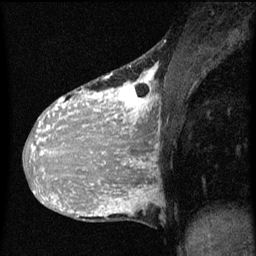
Breast MRI (dynamic contrast-enhanced), one sagittal slice; slice 26 of 60 in the series (ordered by position); dynamic contrast-enhanced series, image 2 of 3 at this slice position (ordered by acquisition); 1.5 T; TE 4.2 ms, TR 8 ms; 2 mm slice thickness; 256 × 256 image matrix, field of view 180 × 180 mm. Patient: female, 36 years.
Annotated regions visible in this slice (semi-automatically segmented with operator editing):
- analysis volume of interest (the breast-tissue region the enhancement analysis was run in; not a lesion): box from (x=32, y=68) to (x=161, y=161) px
- tumour enhancement mask (voxels above the 70 % enhancement threshold inside the analysis volume of interest): (x=32, y=68)–(x=159, y=161)